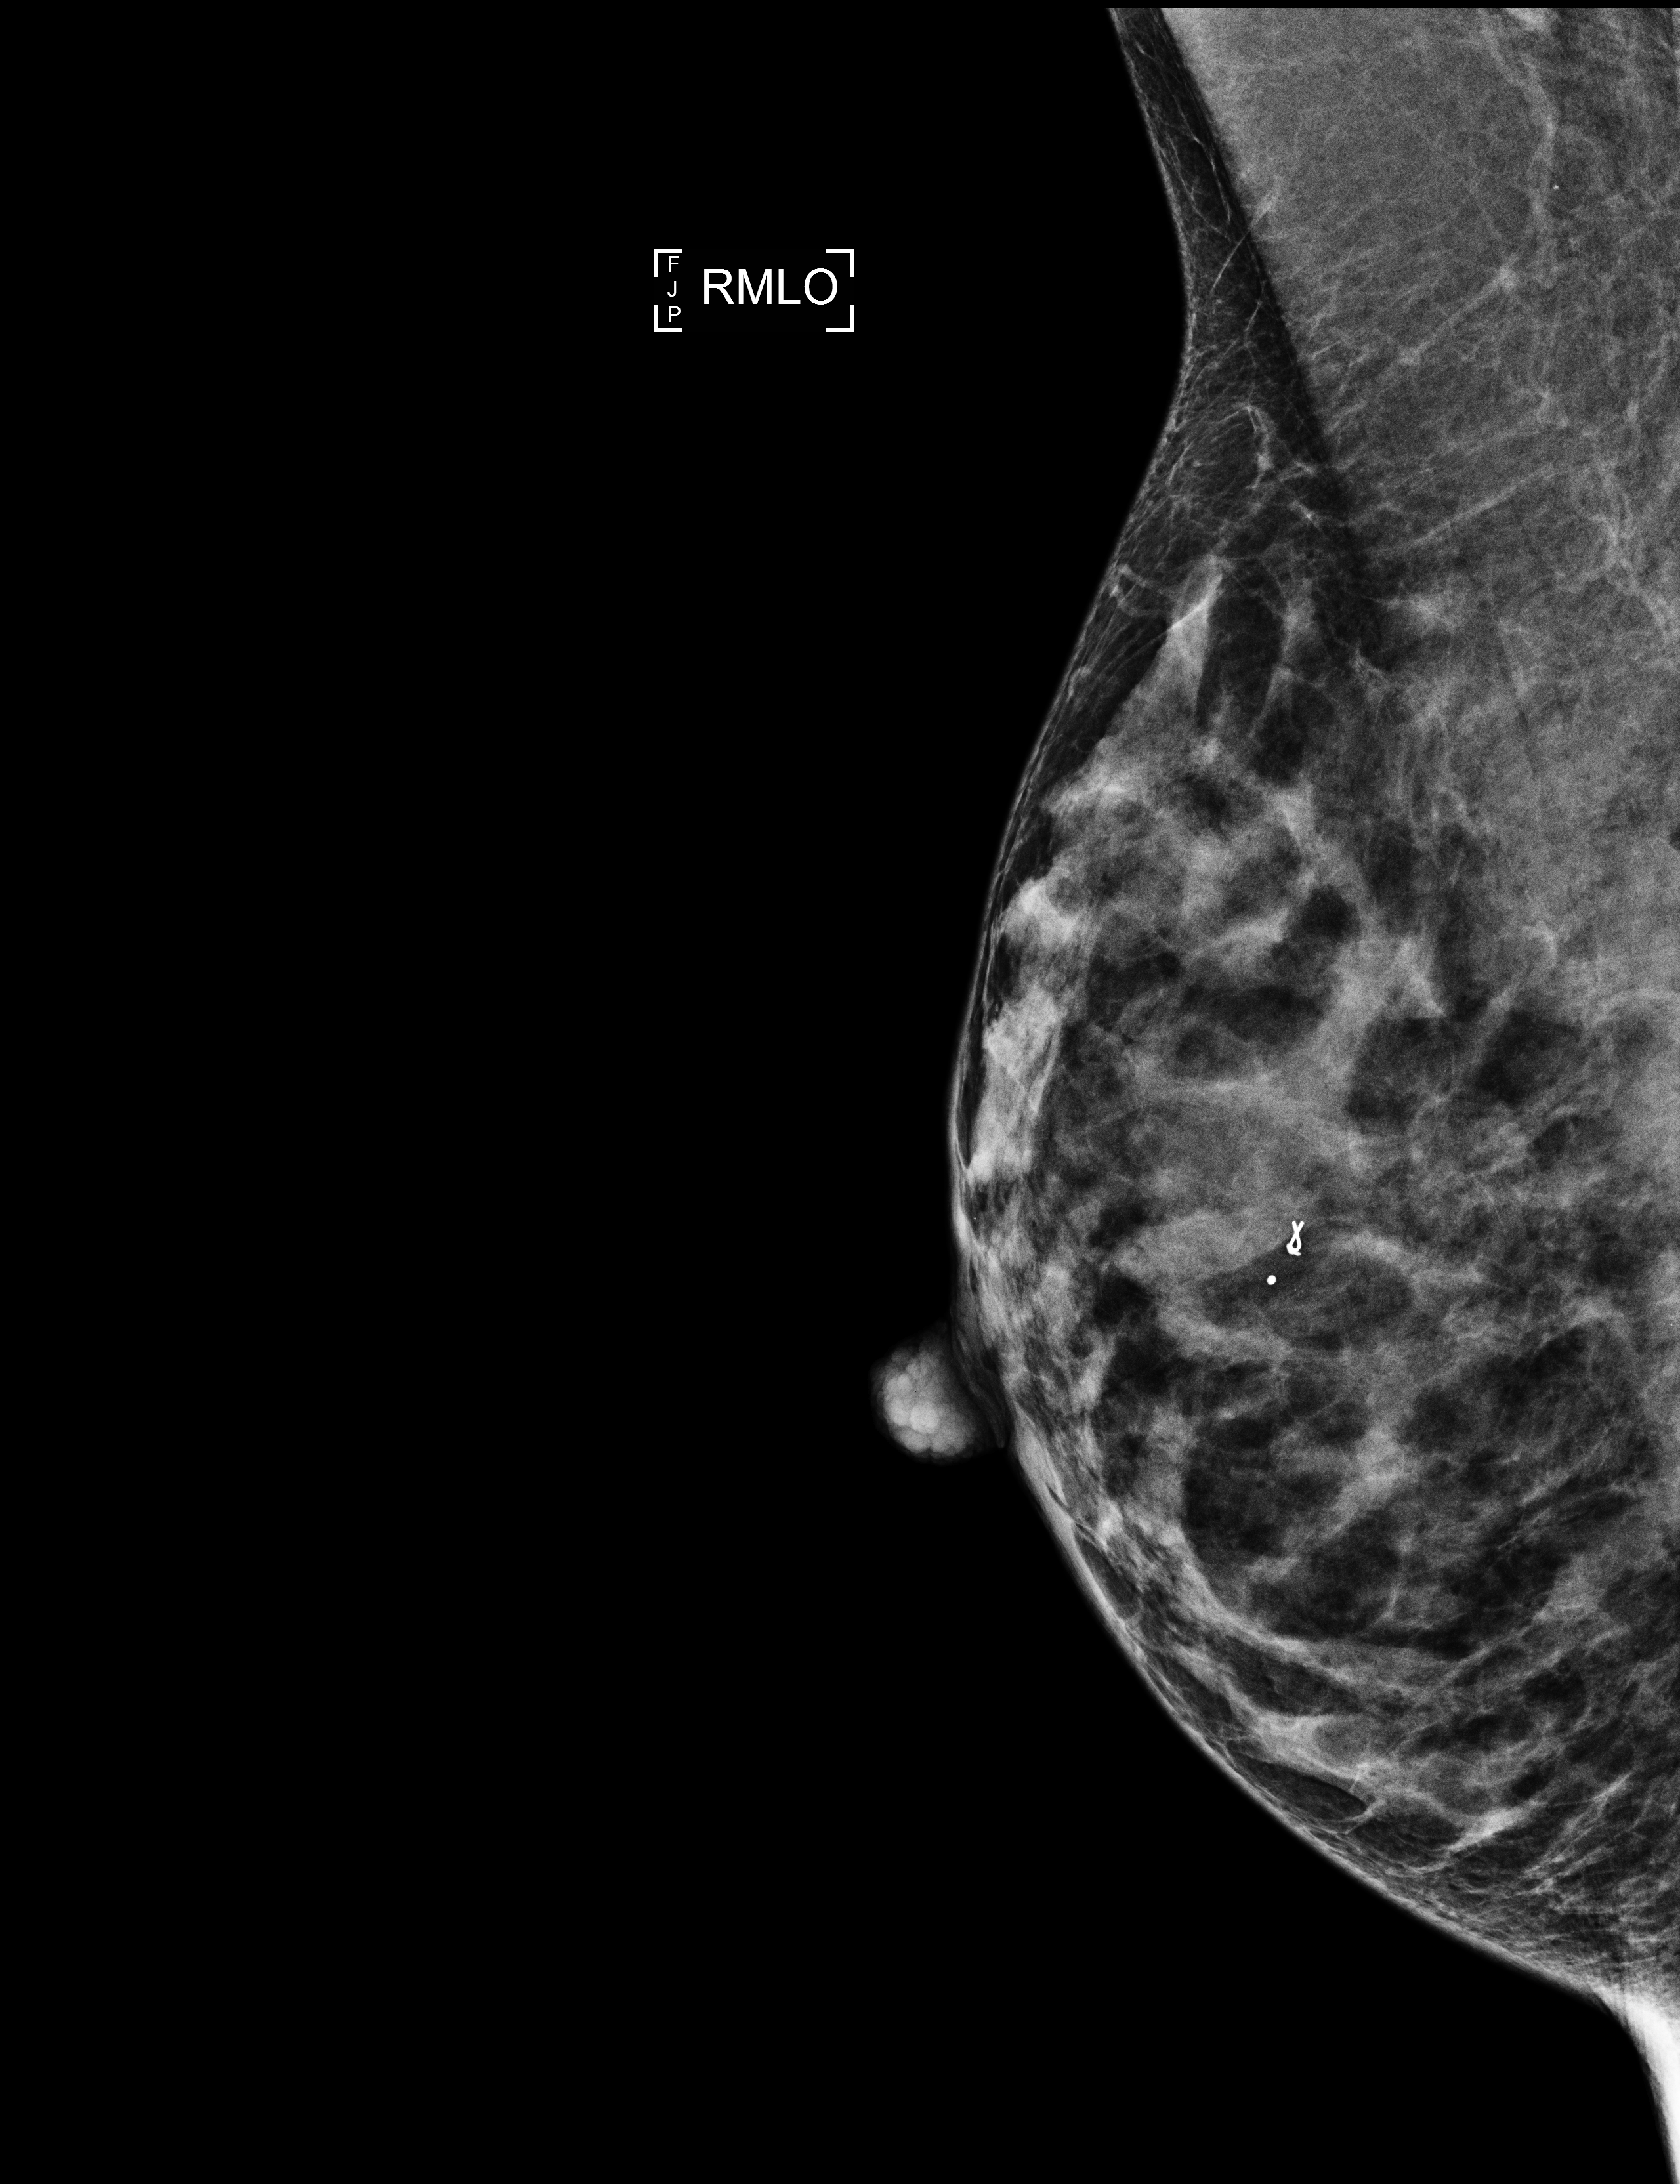
Digital mammogram (FFDM); right breast; medio-lateral oblique projection; screening examination; compressed breast thickness 32 mm; system: Selenia Dimensions. Patient: female, 53 years.
- BI-RADS breast density category at the screening exam (both breasts, scale 1–4): 4
- final BI-RADS assessment for this screening round (tomosynthesis exam, both breasts): category 2
- recall: no recall after this screen